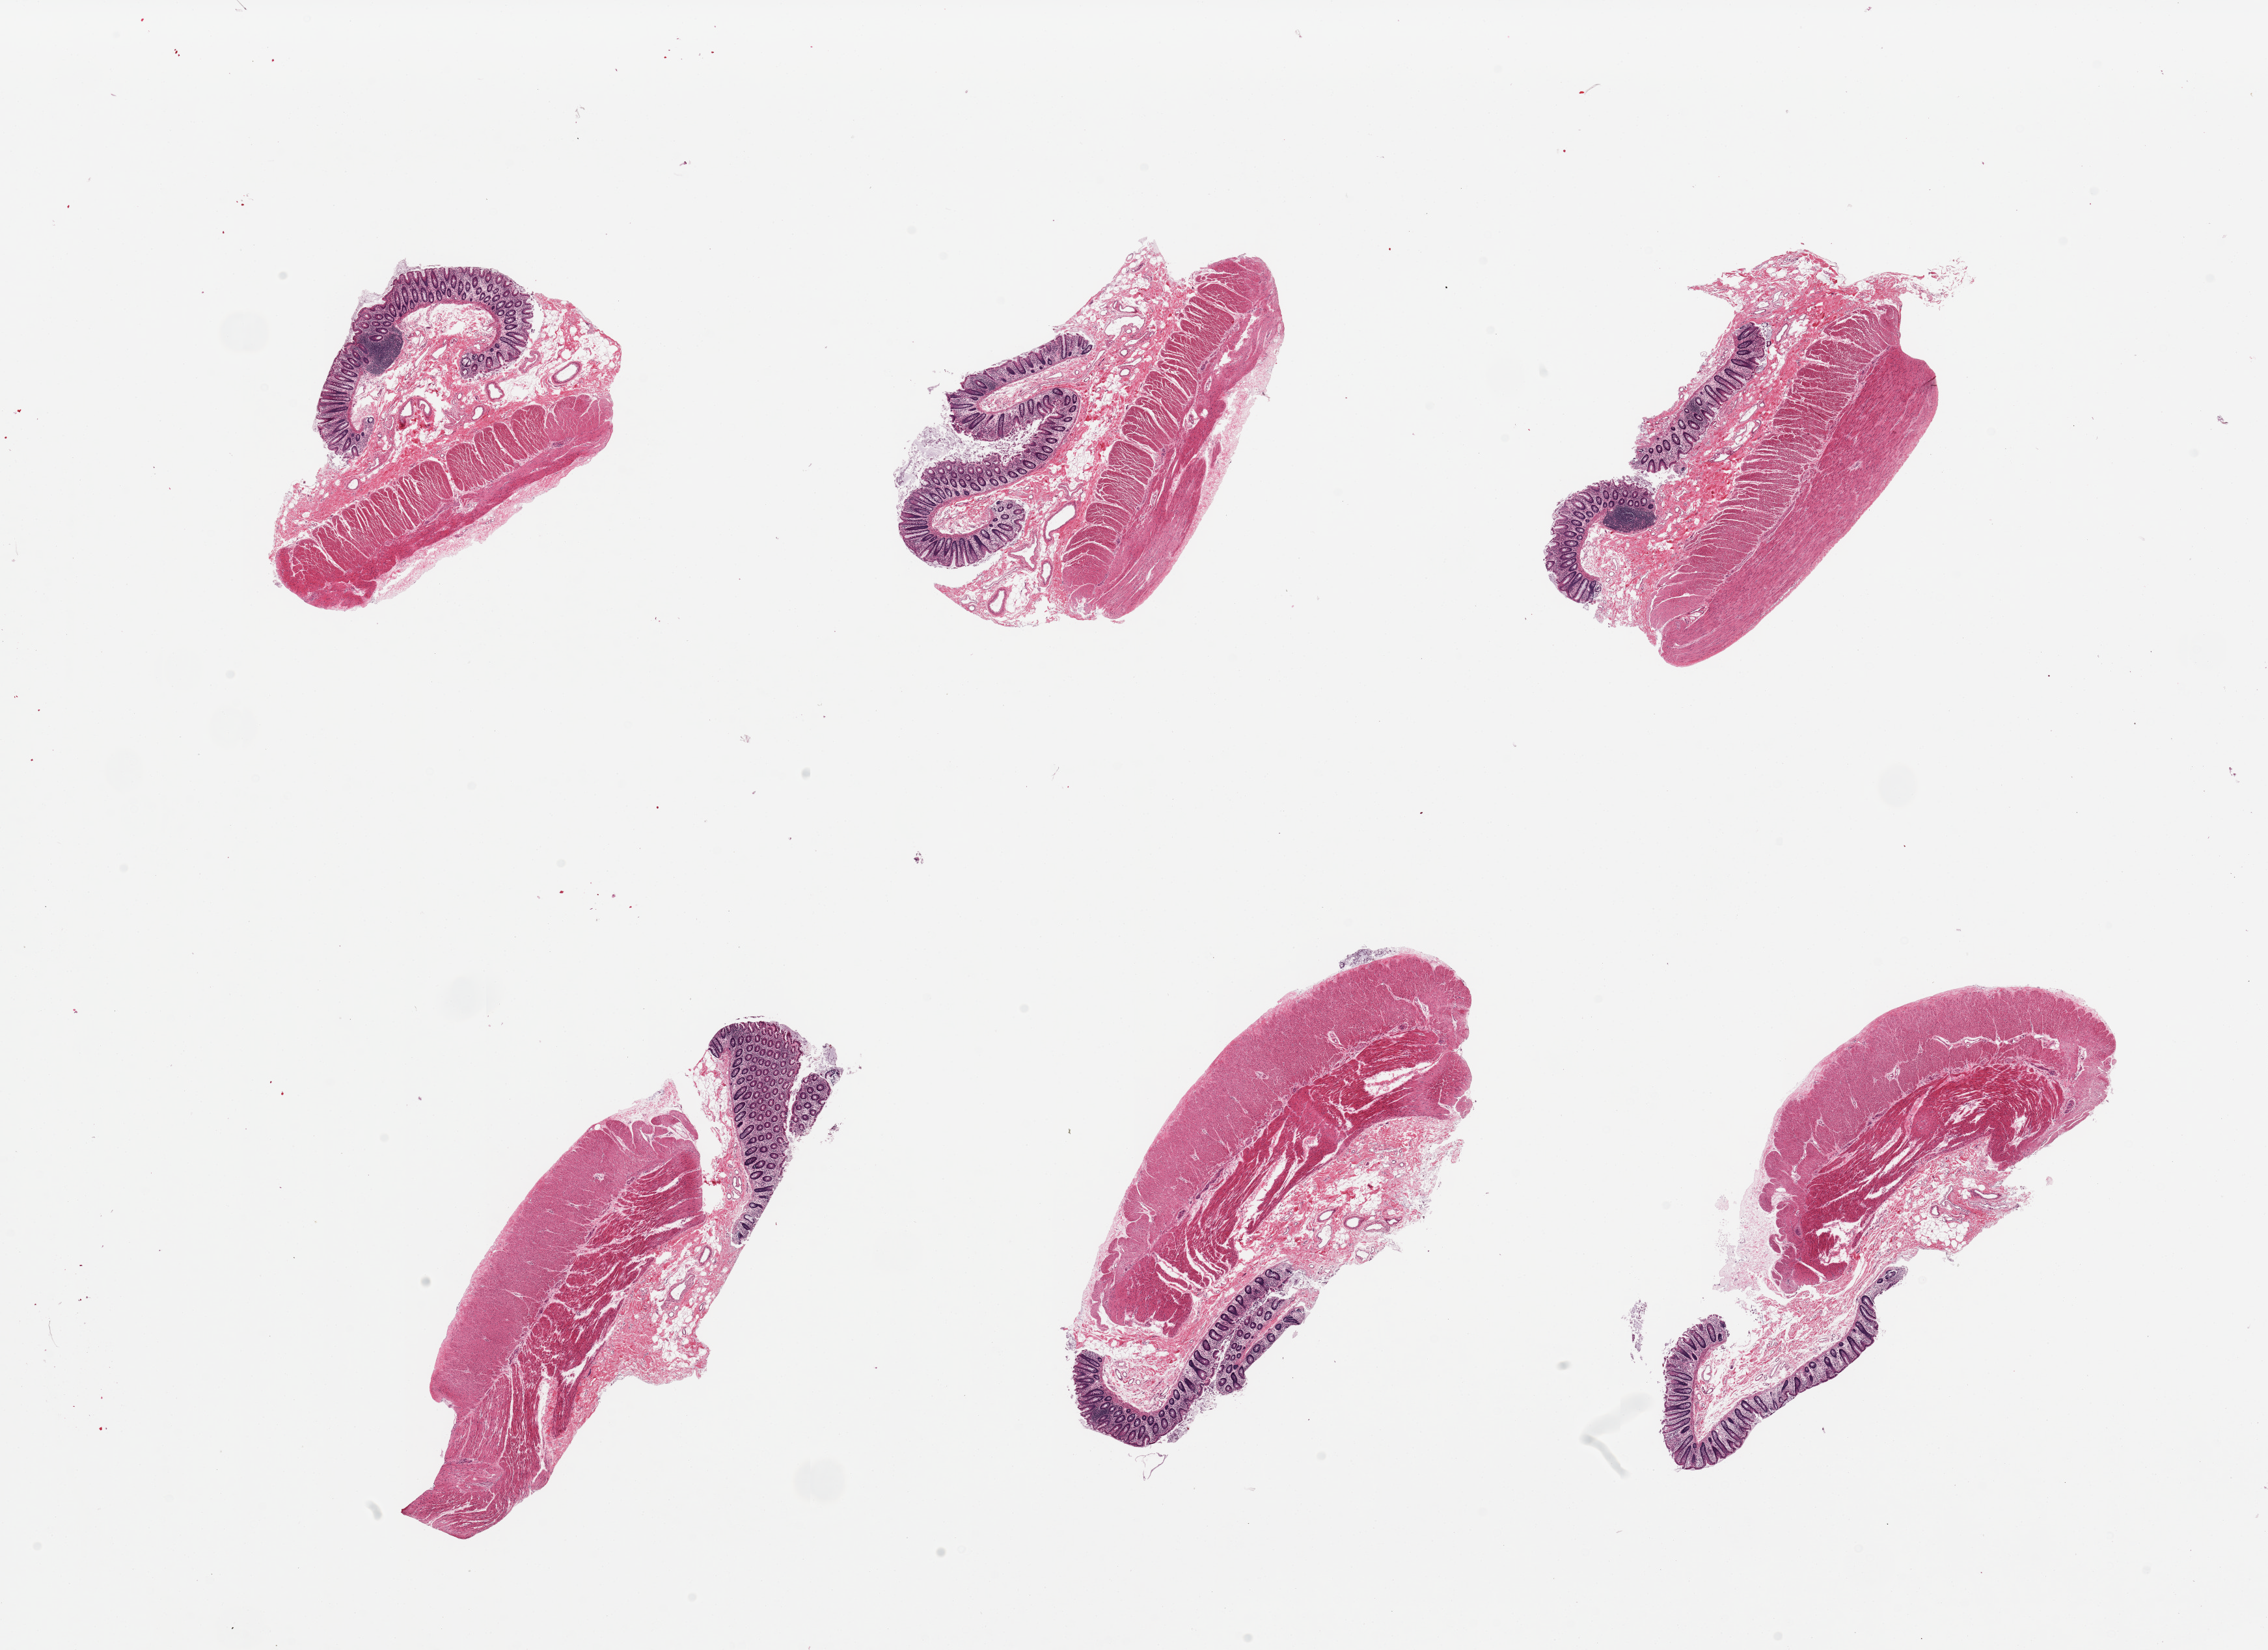
Whole-slide image, H&E stain, whole scanned area (about 27.6 x 20.1 mm, slide scanned at 20x) shown as a low-resolution overview. PAXgene-fixed paraffin-embedded (PFPE) section. Section of transverse colon (target tissue). Donor tissue sample. Female donor.
Pathologist's review note for this sample: 6 pieces, moderately well preserved, some foci approach autolysis score 2. Mucosa is 0.3-0.6mm, ~10% total thickness.